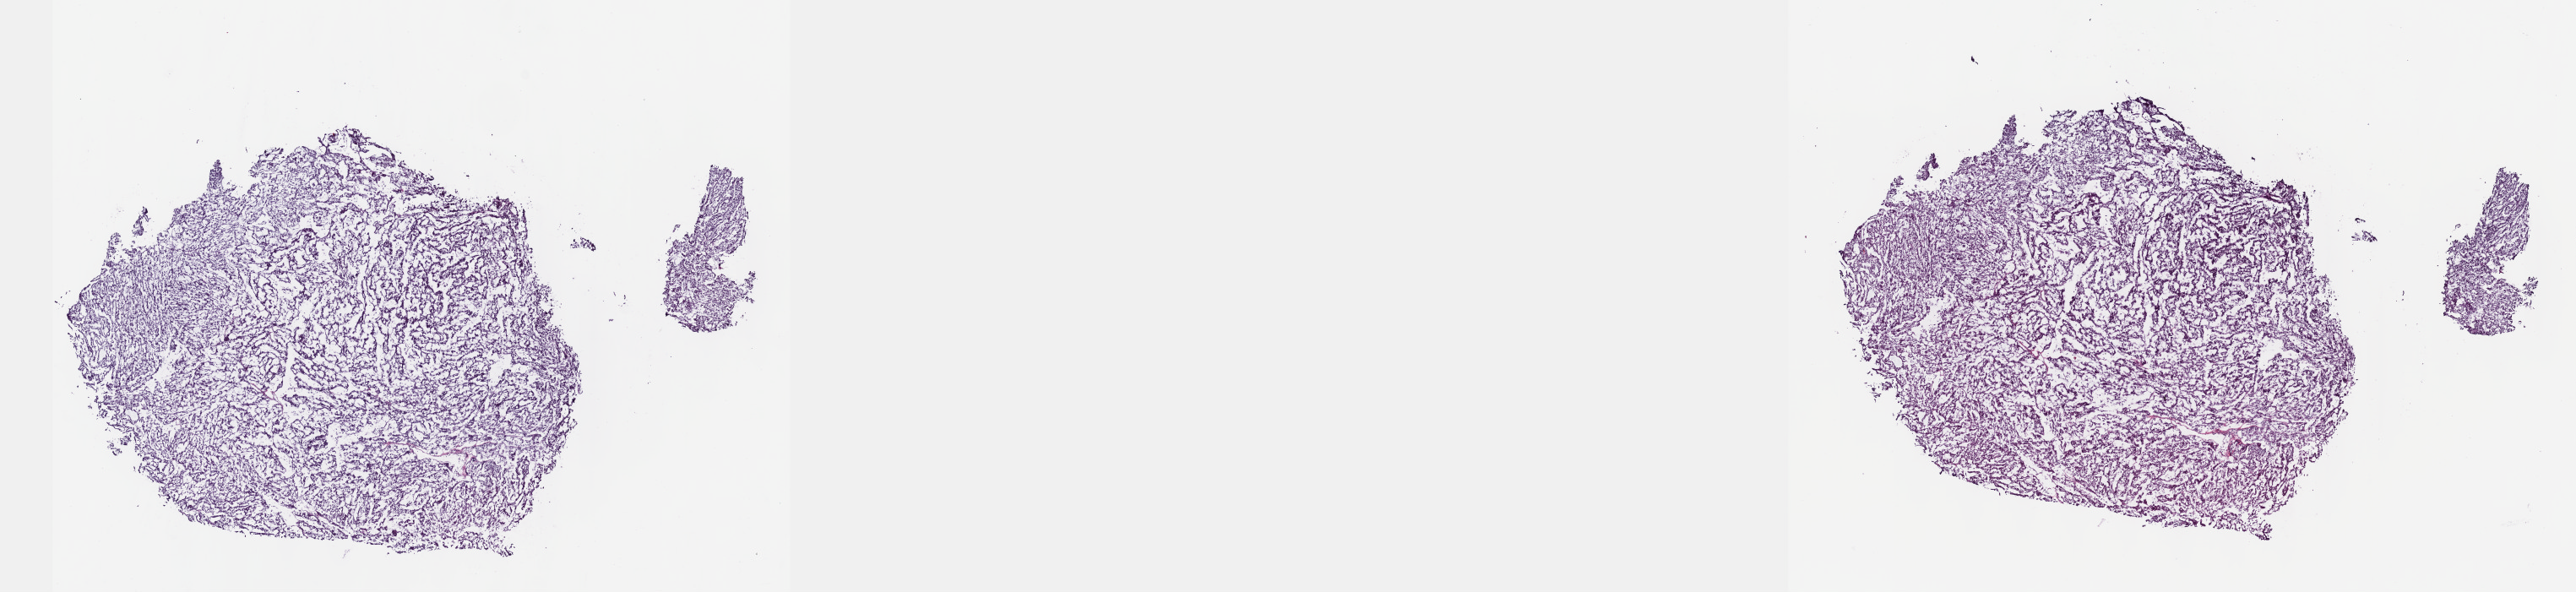
Whole-slide histology image, Hematoxylin and eosin (H&E) stained — low-resolution overview of the scanned area, about 24.6 x 5.7 mm (acquisition: 40x scan). Frozen section from the top of the tissue portion. Sample: primary tumour, kidney. Male patient; age at initial diagnosis 61 years. Pathologist review of this section (percent, as recorded): tumour cells 90%, tumour nuclei 95%, normal cells 0%, stromal cells 8%, necrosis 2%. Inflammatory infiltration, as recorded: lymphocyte infiltration 5%, monocyte infiltration 0%, neutrophil infiltration 0%.
• pathologic diagnosis: Papillary adenocarcinoma, NOS
• AJCC pathologic stage: I (7th edition)
• TNM: T1a NX MX